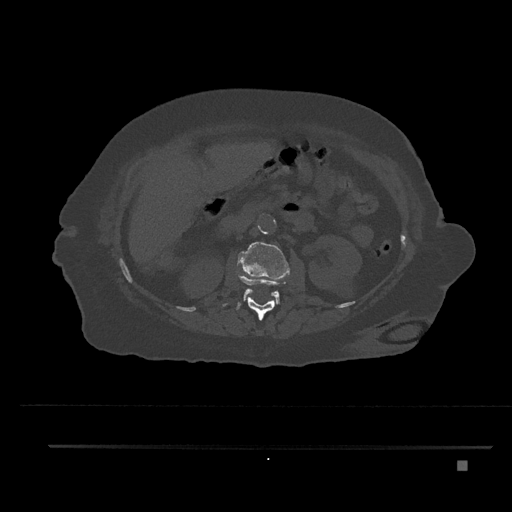
CT including the spine, one axial slice; slice 206 of 797 in the series (ordered by position); bone window (W 1800 / L 400 HU); 0.5 mm slice thickness; 512 × 512 image matrix. Female patient, age 76 years. From the clinical record (not read from this slice): primary cancer: lung.
Outlined on this slice (semi-automatic segmentation, software-assisted and operator-edited):
- L1 vertebra: bounding box <222,274,286,321> (left, top, right, bottom; pixels)
- L2 vertebra: <238,242,290,304>